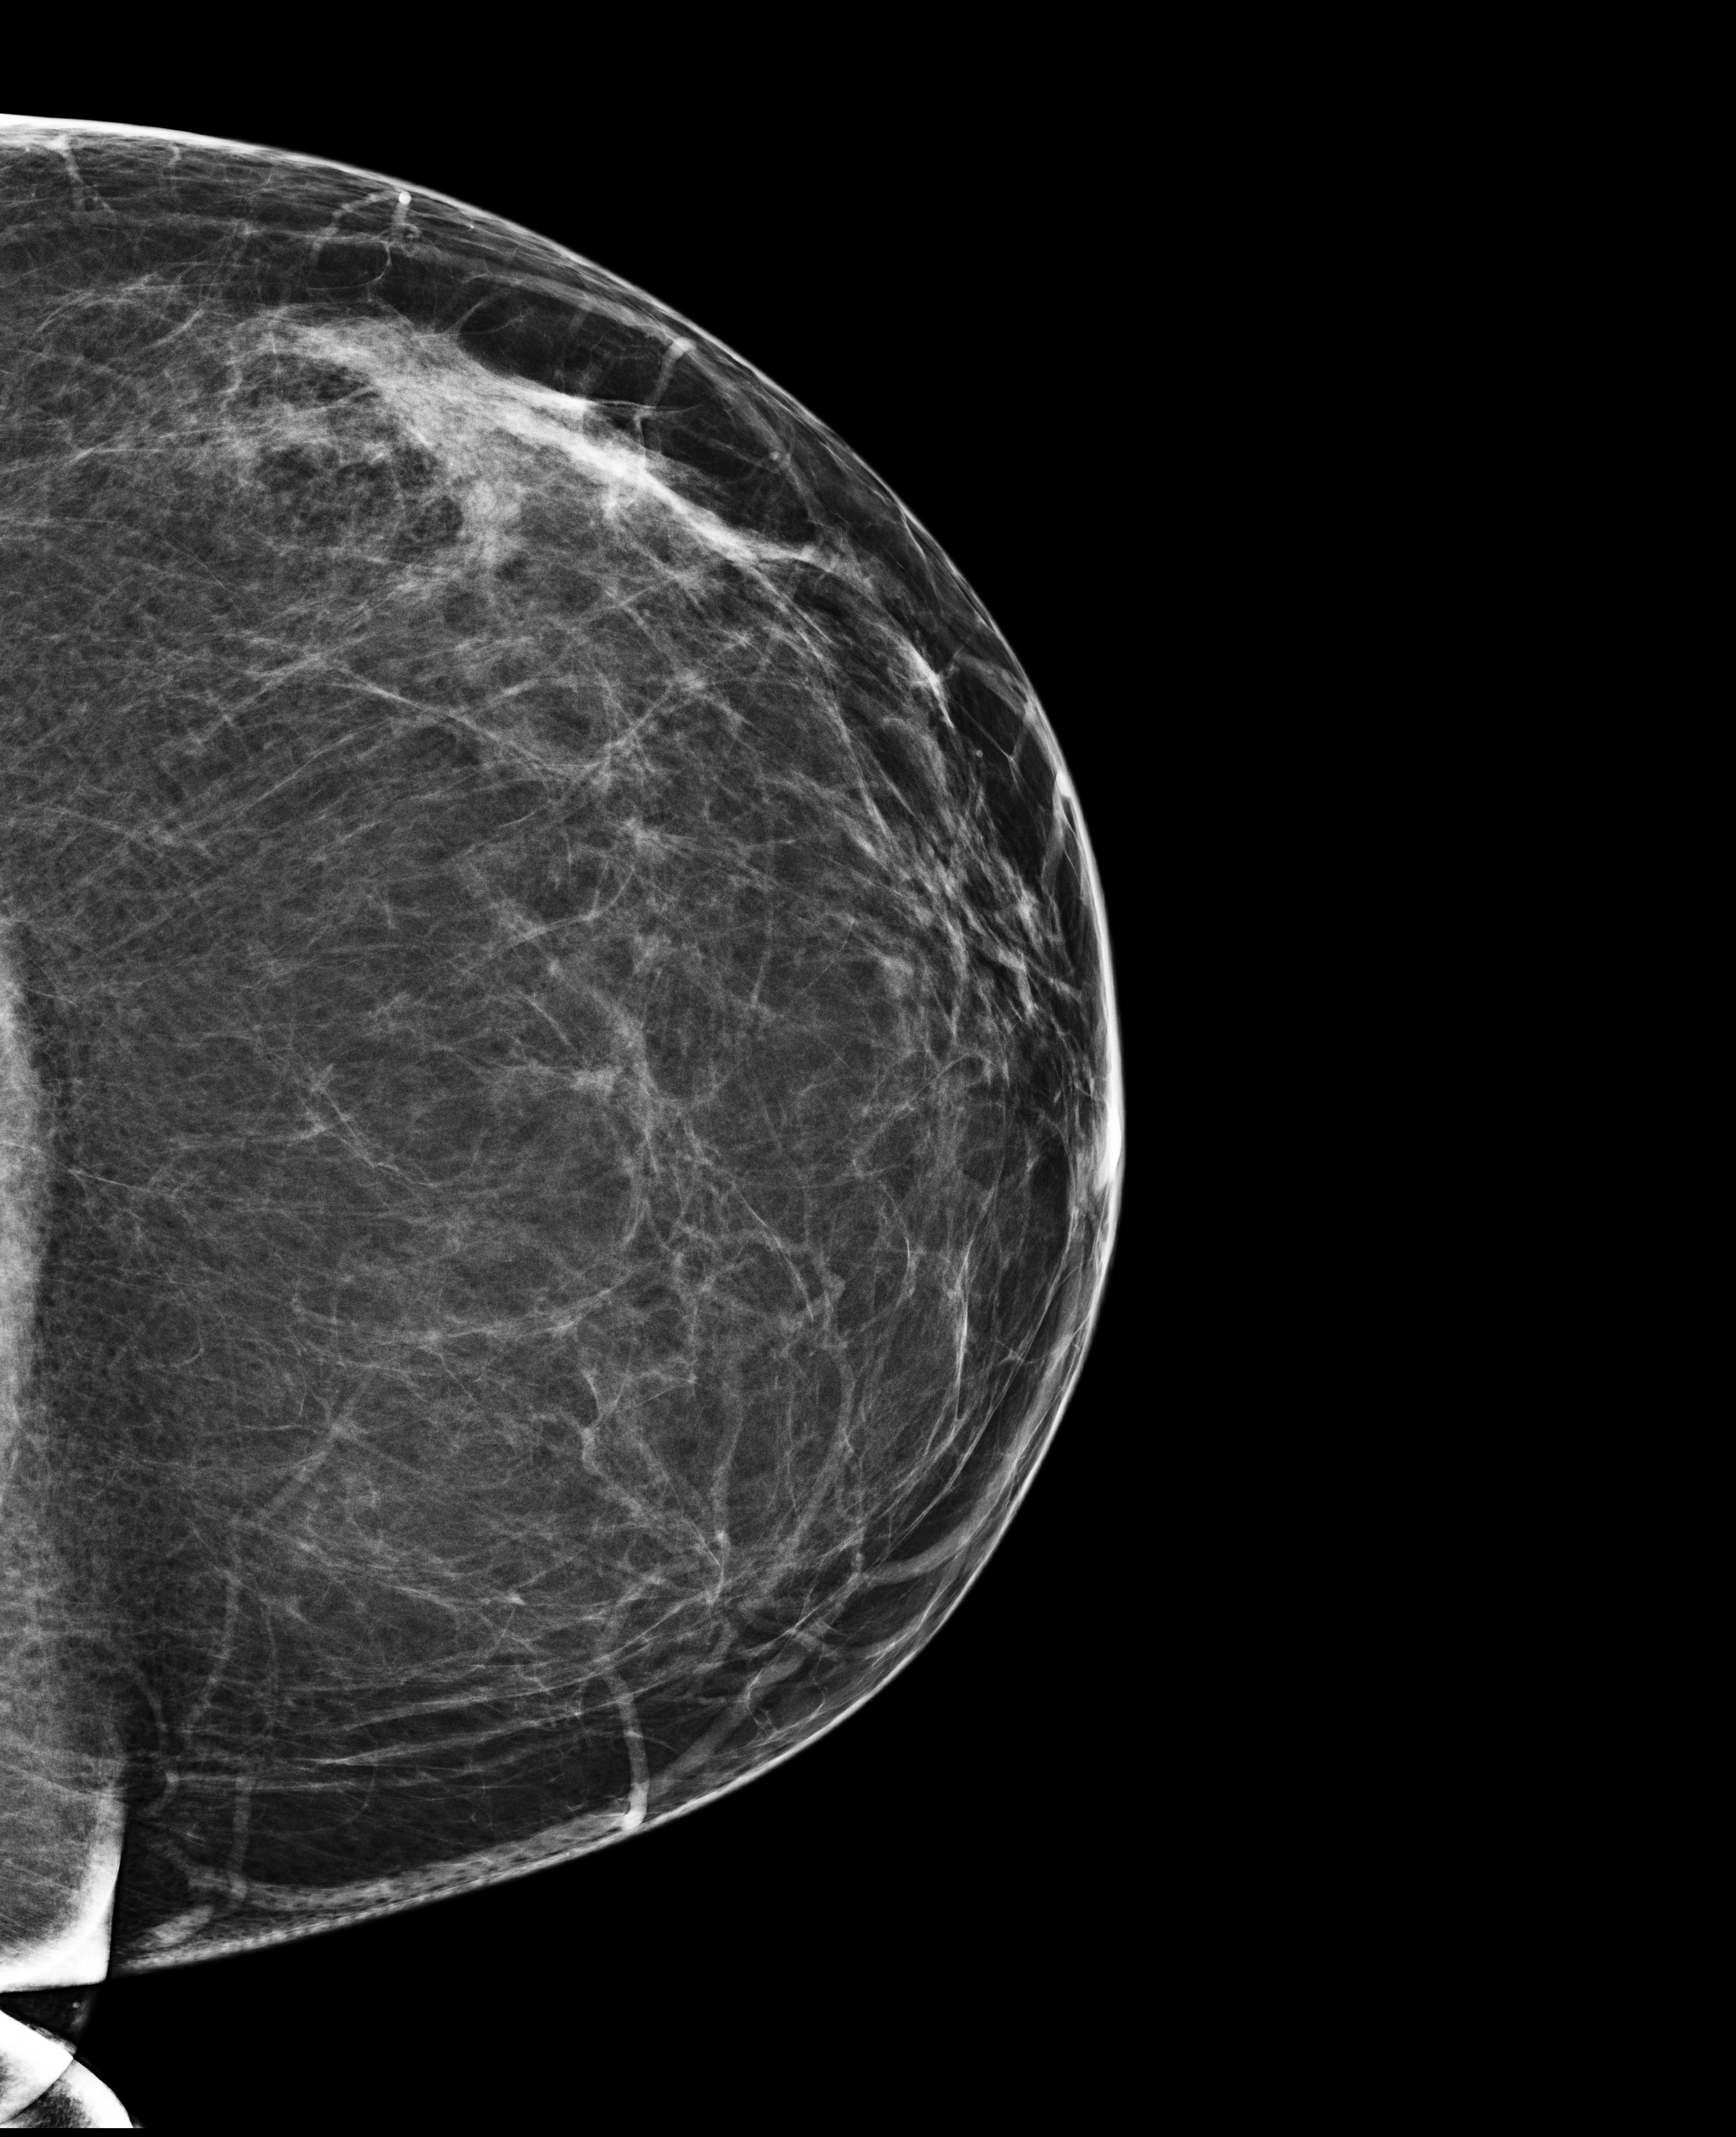
Full-field digital mammogram (FFDM), left breast, cranio-caudal projection, annual screening mammography examination. Female patient, age 52 years.
- BI-RADS breast density category at the screening exam (both breasts, scale 1–4): 2
- final BI-RADS category for the screening round (tomosynthesis exam, both breasts): category 2
- recall: no recall after this screen